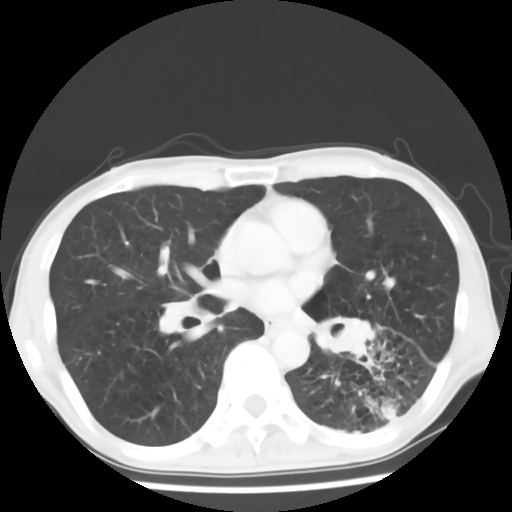
Chest CT, one axial slice. Position 31 of 64 along the scan axis. 120 kVp. Lung window (W 1500 / L -600 HU). 5 mm slice thickness. 512 × 512 image matrix, field of view 313 × 313 mm. Male patient, age 68 years. From the clinical record (not read from this slice): clinical TNM (as recorded): T4 N0 M0.
Structures marked on this image (rectangle marked by the reading radiologist):
- lung tumour (recorded histology: squamous cell carcinoma): bounding box <316,311,378,359> (left, top, right, bottom; pixels)